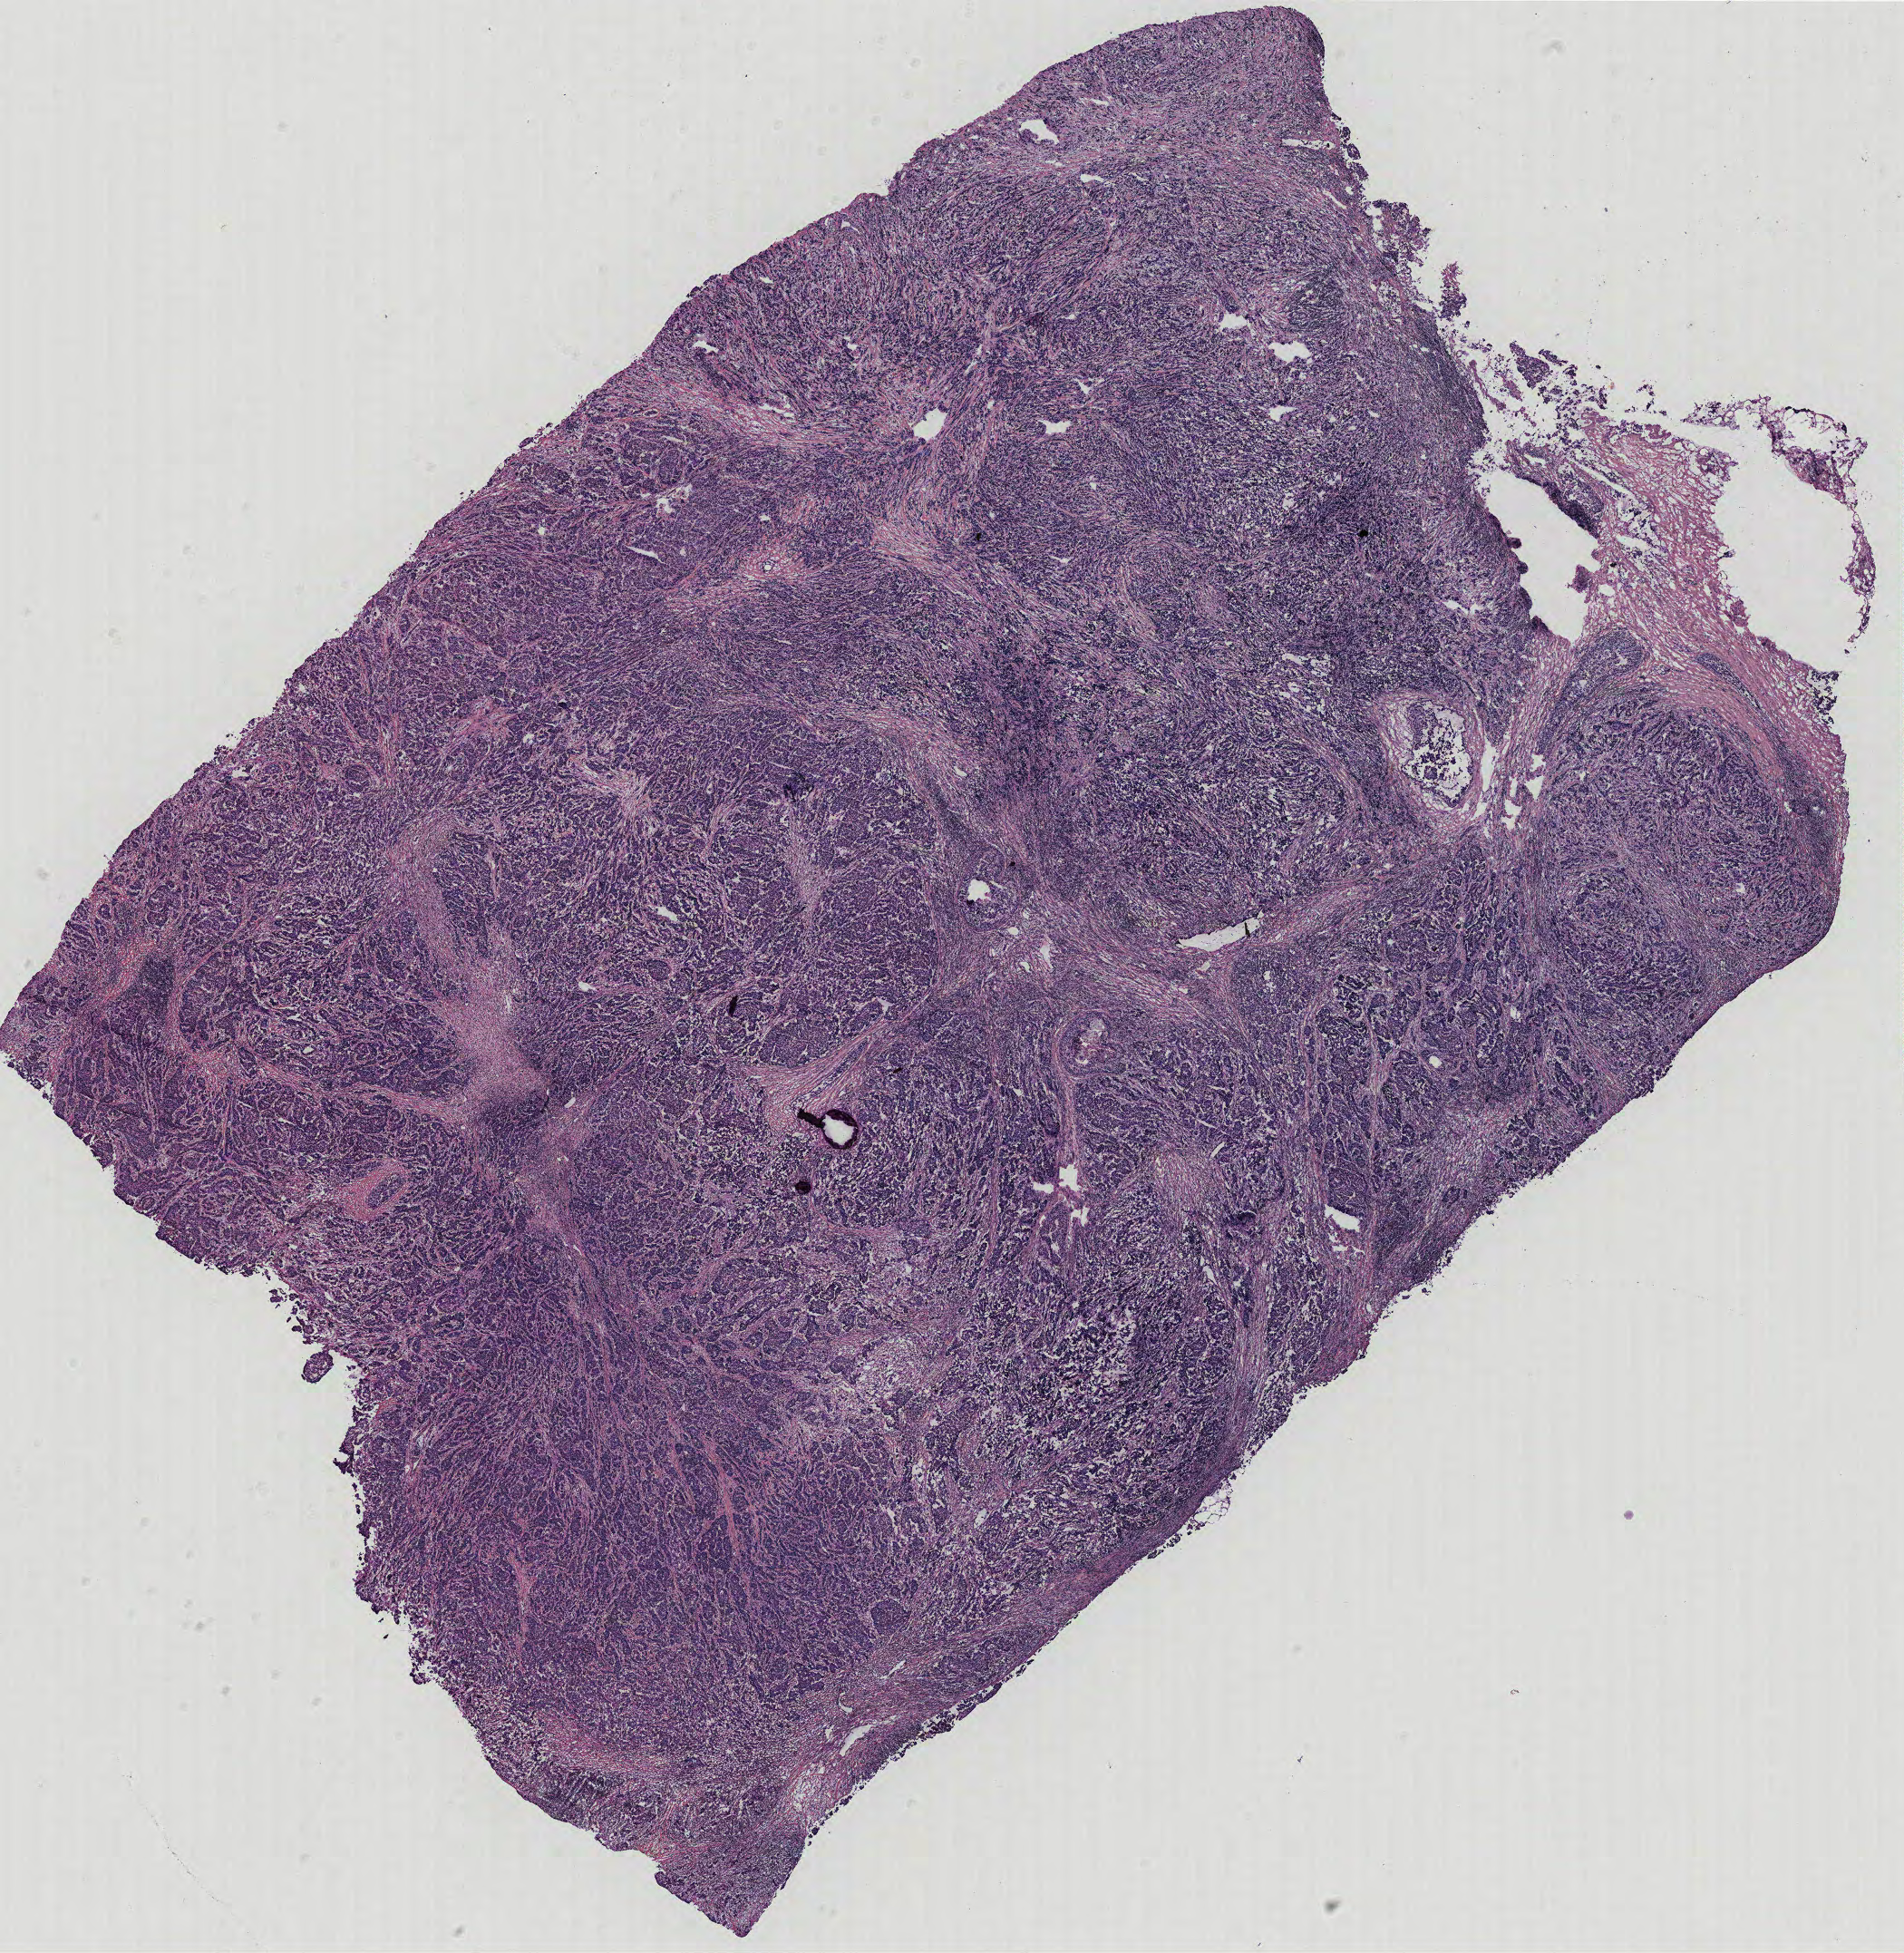
Whole-slide histology image, Hematoxylin and eosin (H&E) stained, a low-resolution overview of the entire scanned area, about 16.8 x 17.2 mm; breast, tissue type not recorded. Female, 36 y/o.
Patient diagnosis: Infiltrating duct carcinoma, NOS.